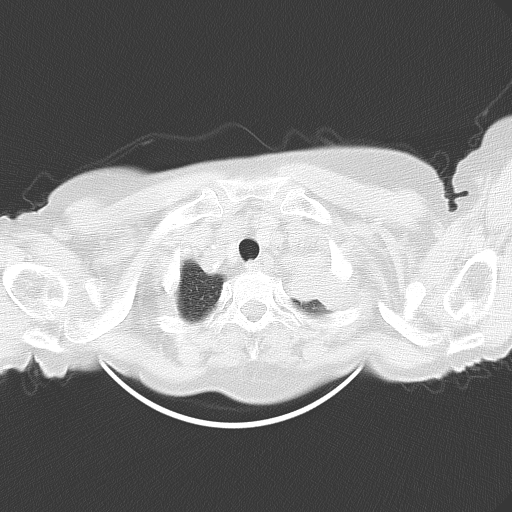
Chest CT, one axial slice. 120 kVp. Lung window (W 1500 / L -600 HU). 5 mm slice thickness. 512 × 512 image matrix. Patient: female, 71 years. From the clinical record (not read from this slice): clinical TNM (as recorded): T3 N3 M0.
Structures marked on this image (rectangle marked by the reading radiologist):
- lung tumour (recorded histology: adenocarcinoma): bounding box [x1, y1, x2, y2] px = [284, 249, 363, 319]